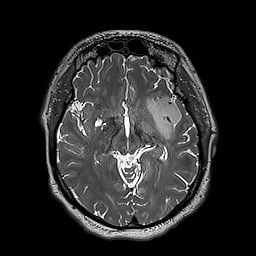
Brain MRI from a brain-tumour surgery series, one axial slice. Position 111 of 192 along the scan axis. 256 × 256 image matrix. Case-level facts recorded for this patient, not image findings: histopathology: Astrocytoma; WHO grade: 3; IDH mutation: yes.
Outlined on this slice (manually delineated by an expert):
- tumour: box from (x=147, y=97) to (x=182, y=140) px